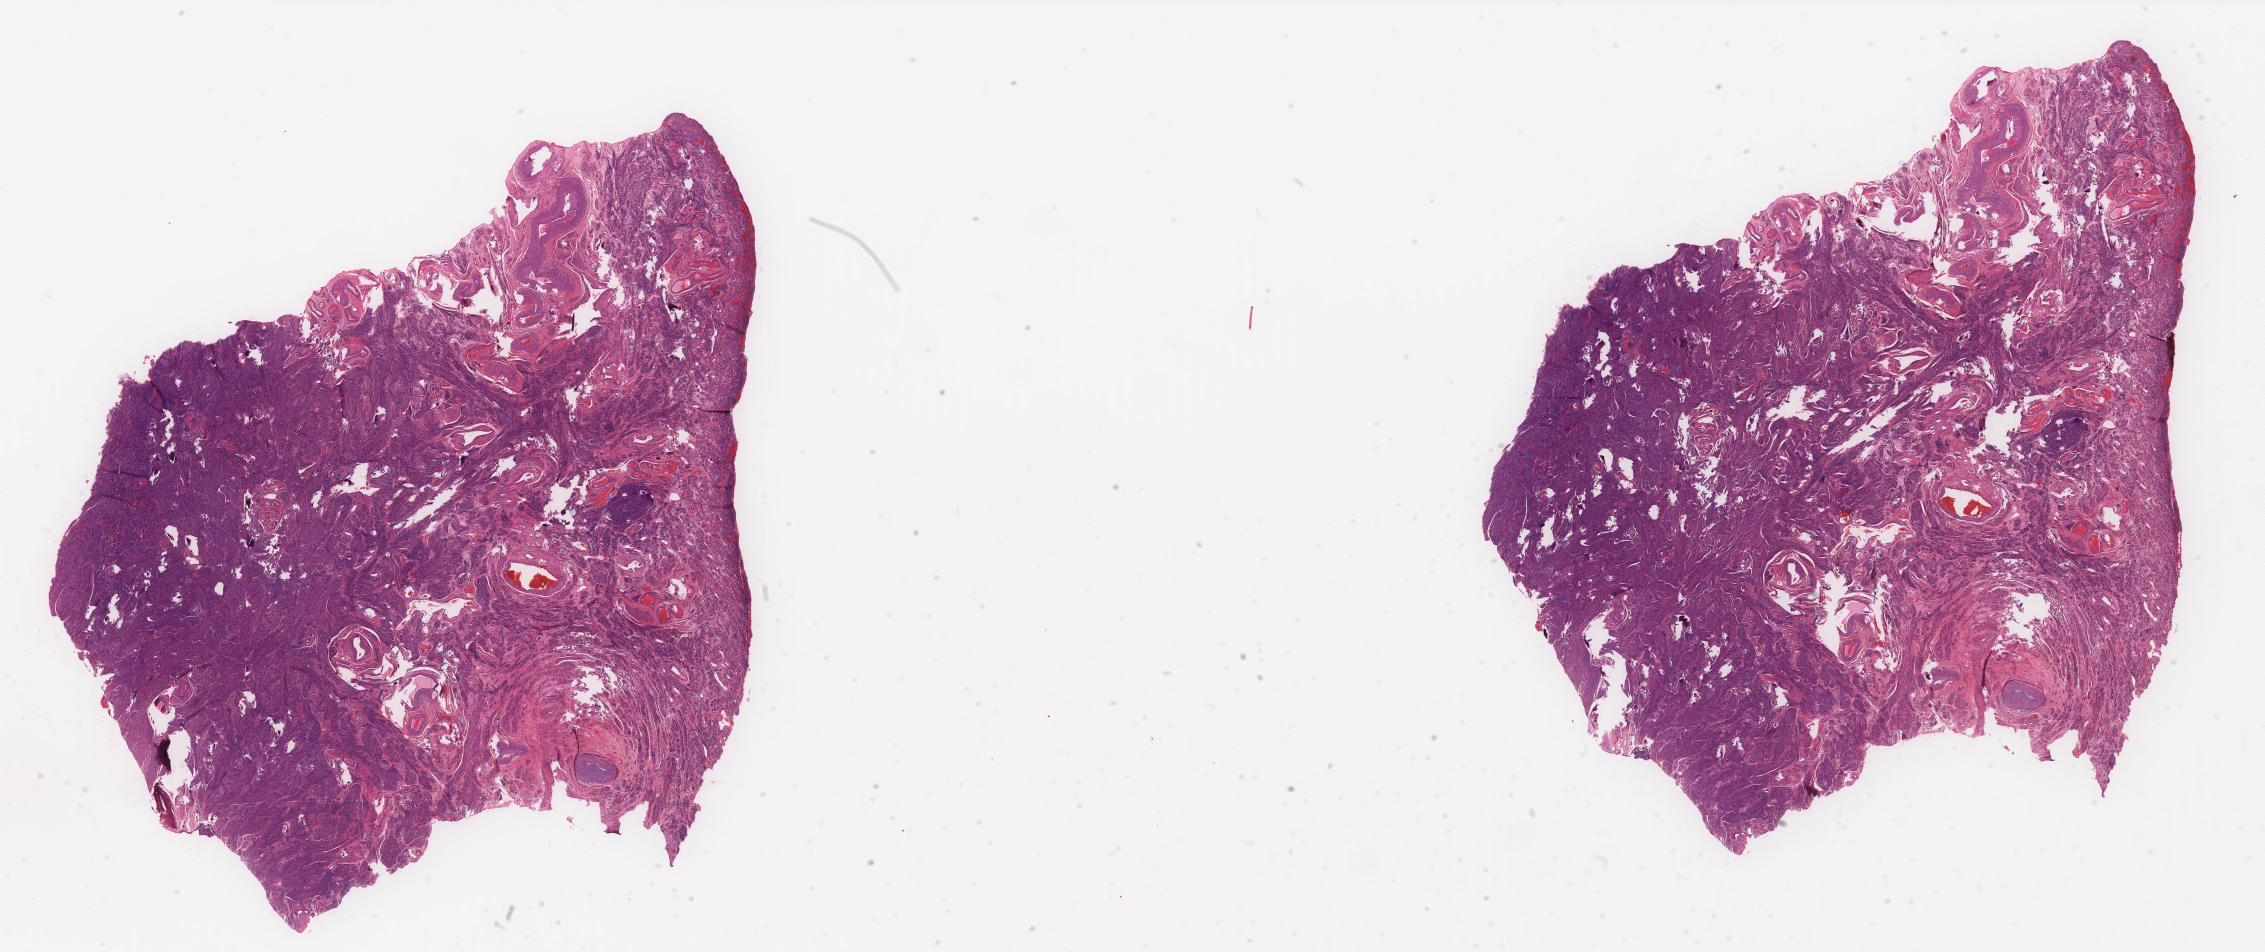
H&E whole-slide image, whole scanned area (about 36.3 x 15.3 mm, acquisition: 40x scan) shown as a low-resolution overview; formalin-fixed paraffin-embedded (FFPE) diagnostic section; sample: primary tumour, uterus. Female patient; age at initial diagnosis 58 years. Histologic grade: G1 (well differentiated).
Lymph nodes positive (case pathology): 0 of 1 examined. Diagnosis: Endometrioid adenocarcinoma, NOS (endometrium). FIGO stage: IA.